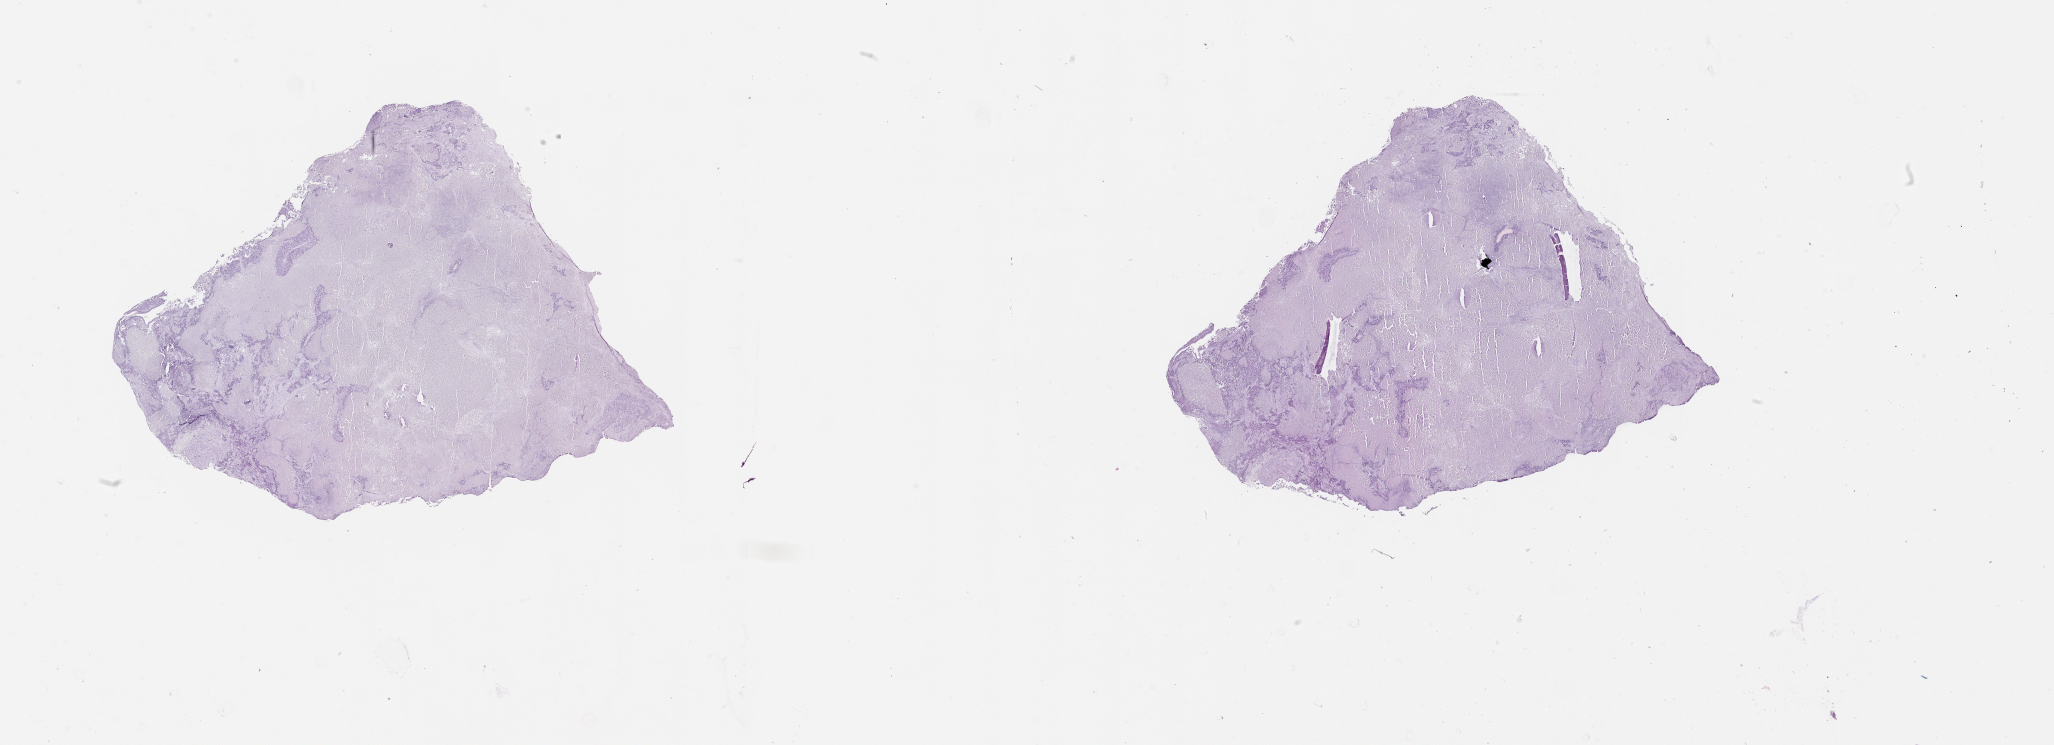
Digitized H&E tissue section (whole slide) — a low-resolution overview of the entire scanned area, about 33.1 x 12.0 mm (slide scanned at 20x); lung, tissue type not recorded.
Patient diagnosis (cohort enrolment): lung adenocarcinoma (lung).